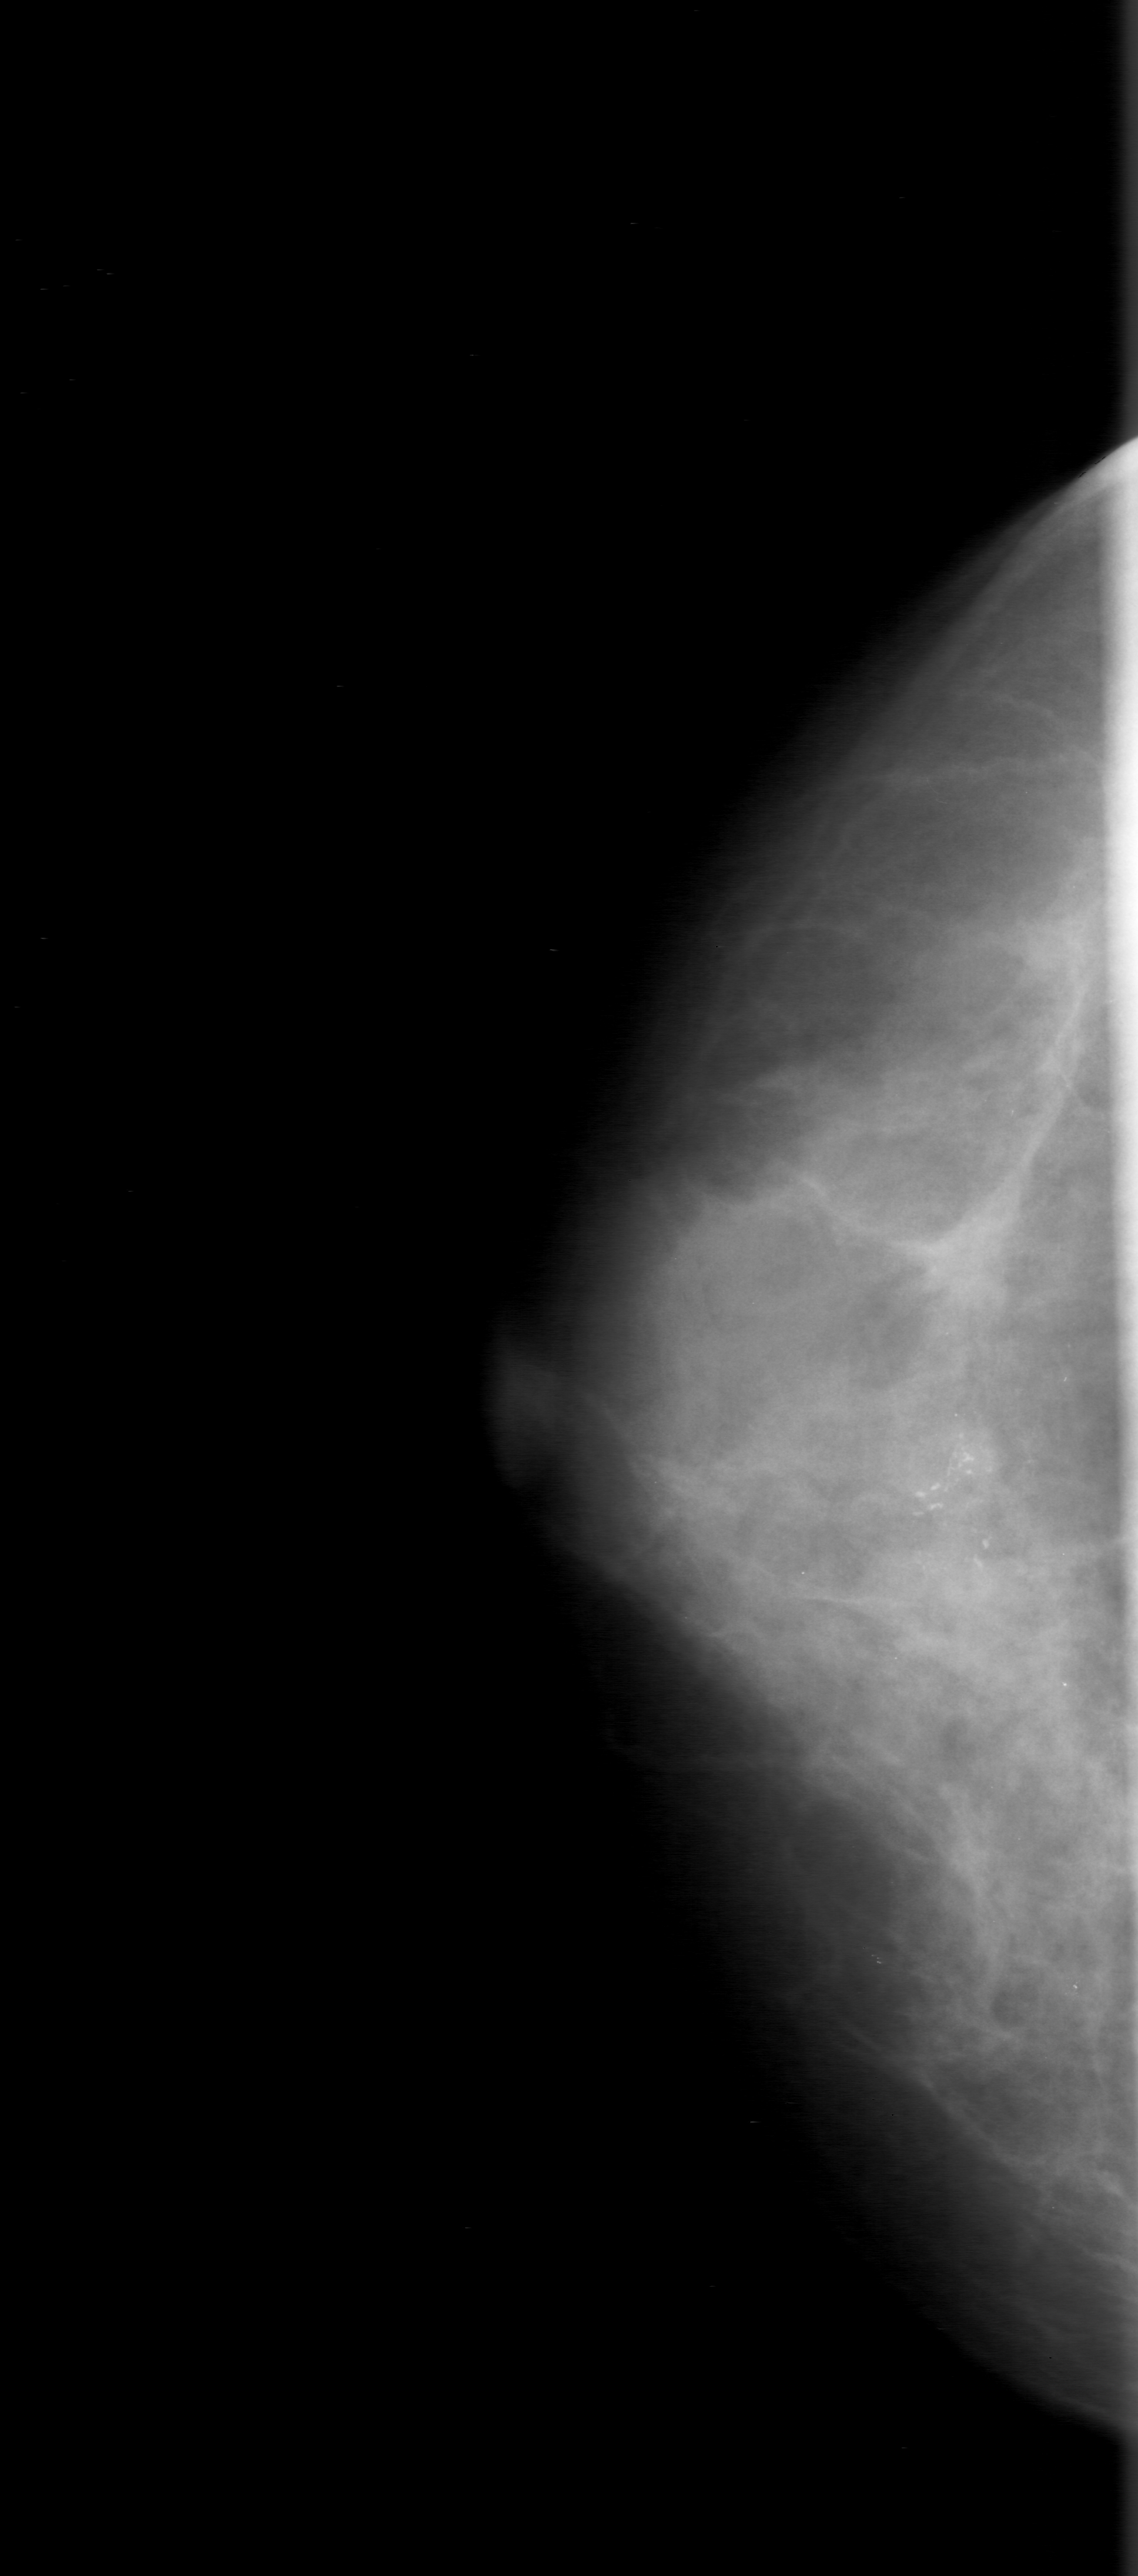
Digitized screen-film mammogram; right breast; craniocaudal (CC) view; BI-RADS breast density category 3 (scale 1–4).
Marked abnormality: calcifications, morphology fine linear branching, distribution clustered; BI-RADS assessment category 3; subtlety rating 5 on a 1 (subtle) to 5 (obvious) scale; pathology result (as recorded, not read from the image): malignant.